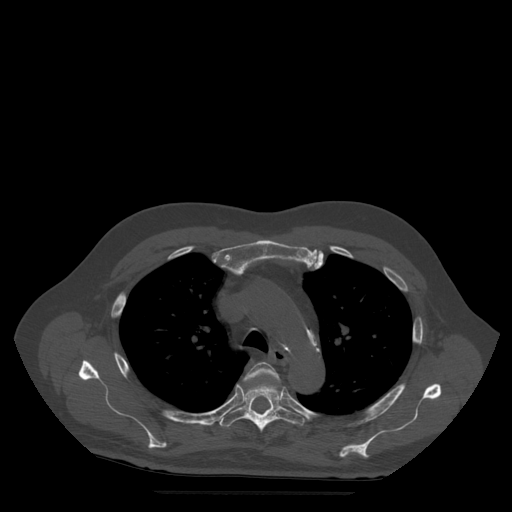
CT including the spine, one axial slice; position 378 of 522 along the scan axis; bone window (W 1800 / L 400 HU); 1.25 mm slice thickness; 512 × 512 image matrix, field of view 420 × 420 mm. Patient age 72 years. Case-level facts recorded for this patient, not image findings: primary cancer: prostate.
Structures marked on this image (semi-automatically segmented with operator editing):
- T4 vertebra: bounding box (x1, y1, x2, y2) in pixels: (244, 363, 280, 381)
- T5 vertebra: (220, 376, 305, 432)